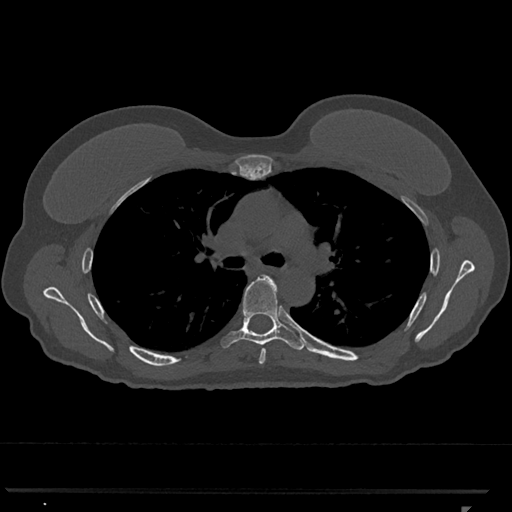
CT including the spine, one axial slice. Reconstruction kernel Br40s/3. Bone window (W 1800 / L 400 HU). 0.5 mm slice thickness. 512 × 512 image matrix. Female patient, age 62 years. From the clinical record (not read from this slice): primary cancer: renal.
Annotated regions visible in this slice (semi-automatically segmented with operator editing):
- T5 vertebra: bounding box [x1, y1, x2, y2] px = [259, 349, 266, 365]
- T6 vertebra: [222, 275, 305, 350]